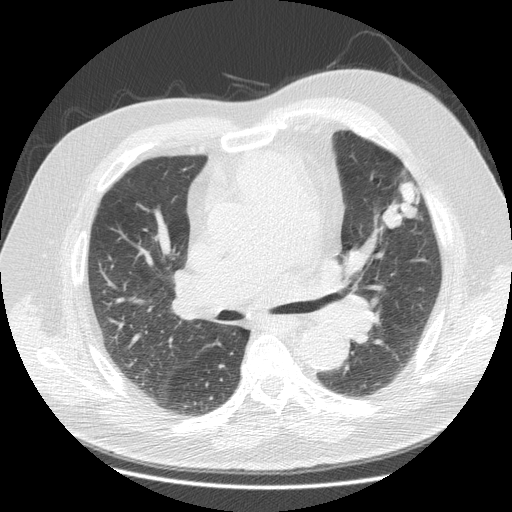
Low-dose screening chest CT, one axial slice; slice 63 of 116 in the series (ordered by position); lung window (W 1500 / L -600 HU); 2.5 mm slice thickness; 512 × 512 image matrix, field of view 390 × 390 mm.
Annotated regions visible in this slice (manually delineated by an expert):
- lesion 1 (tumor, upper lobe of left lung): box from (x=382, y=180) to (x=418, y=229) px